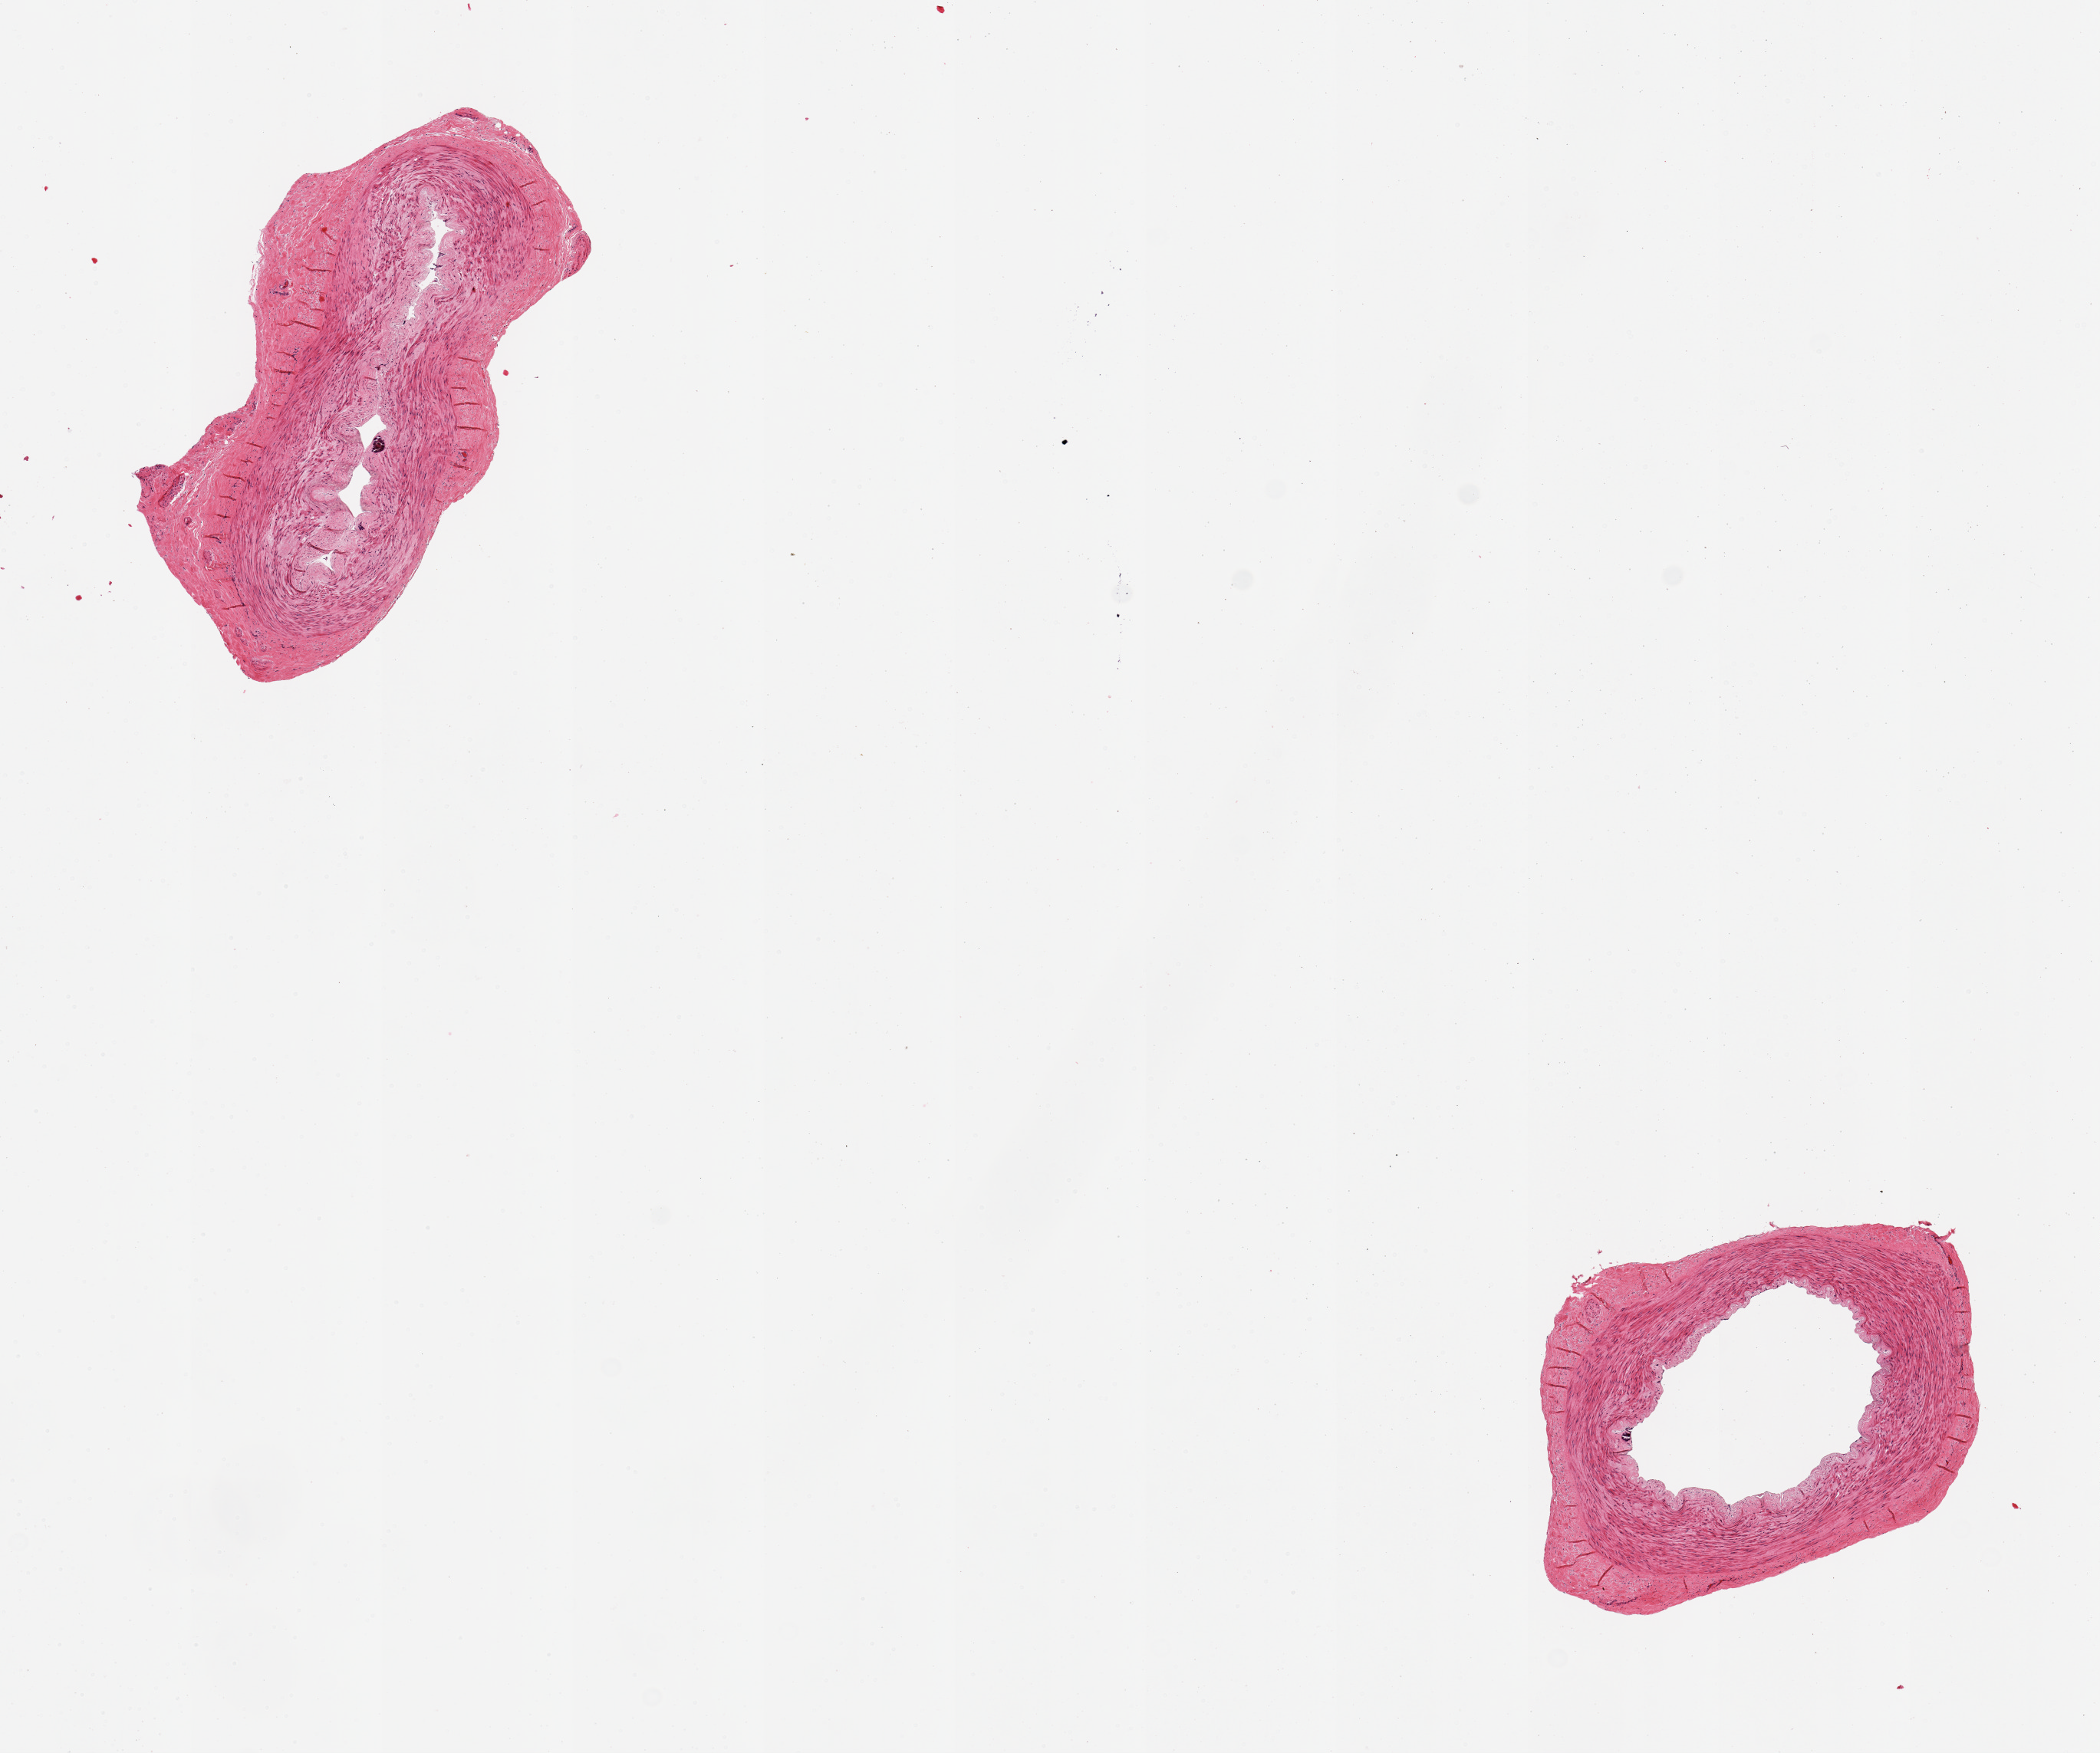
H&E whole-slide image, low-resolution overview of the scanned area, about 10.8 x 9.0 mm. PAXgene-fixed paraffin-embedded (PFPE) section. Section of tibial artery (target tissue). Donor tissue sample. Male donor.
Reviewer comment on this tissue sample: 2 pieces; well dissected; very small focal intimal calcifications.